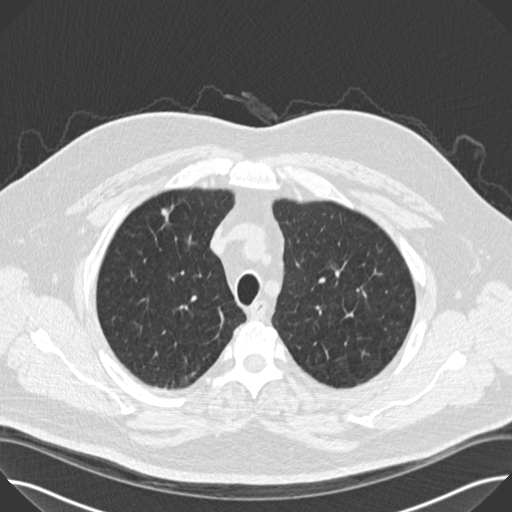
Chest CT (low-dose screening protocol), one axial image; baseline screening round; lung window (W 1500 / L -600 HU); 2 mm slice thickness; slice 128 of 158 in the series; 512 × 512 image matrix. Male participant, aged 65 years at enrolment.
Expert-annotated lung lesion, box from (x=148, y=358) to (x=194, y=414) px. The screening reader recorded 2 non-calcified nodules or masses ≥4 mm on this exam (right upper lobe, right upper lobe); which of them this box marks is not recorded. Official screen result: positive, change unspecified: nodule(s) >= 4 mm or enlarging nodule(s), mass(es), or other non-specific abnormalities suspicious for lung cancer. Lung cancer was diagnosed 47 days after this screen: bronchiolo-alveolar adenocarcinoma, NOS, right upper lobe, moderately differentiated (G2), stage IIA (AJCC 6th edition), 14 mm at pathology.